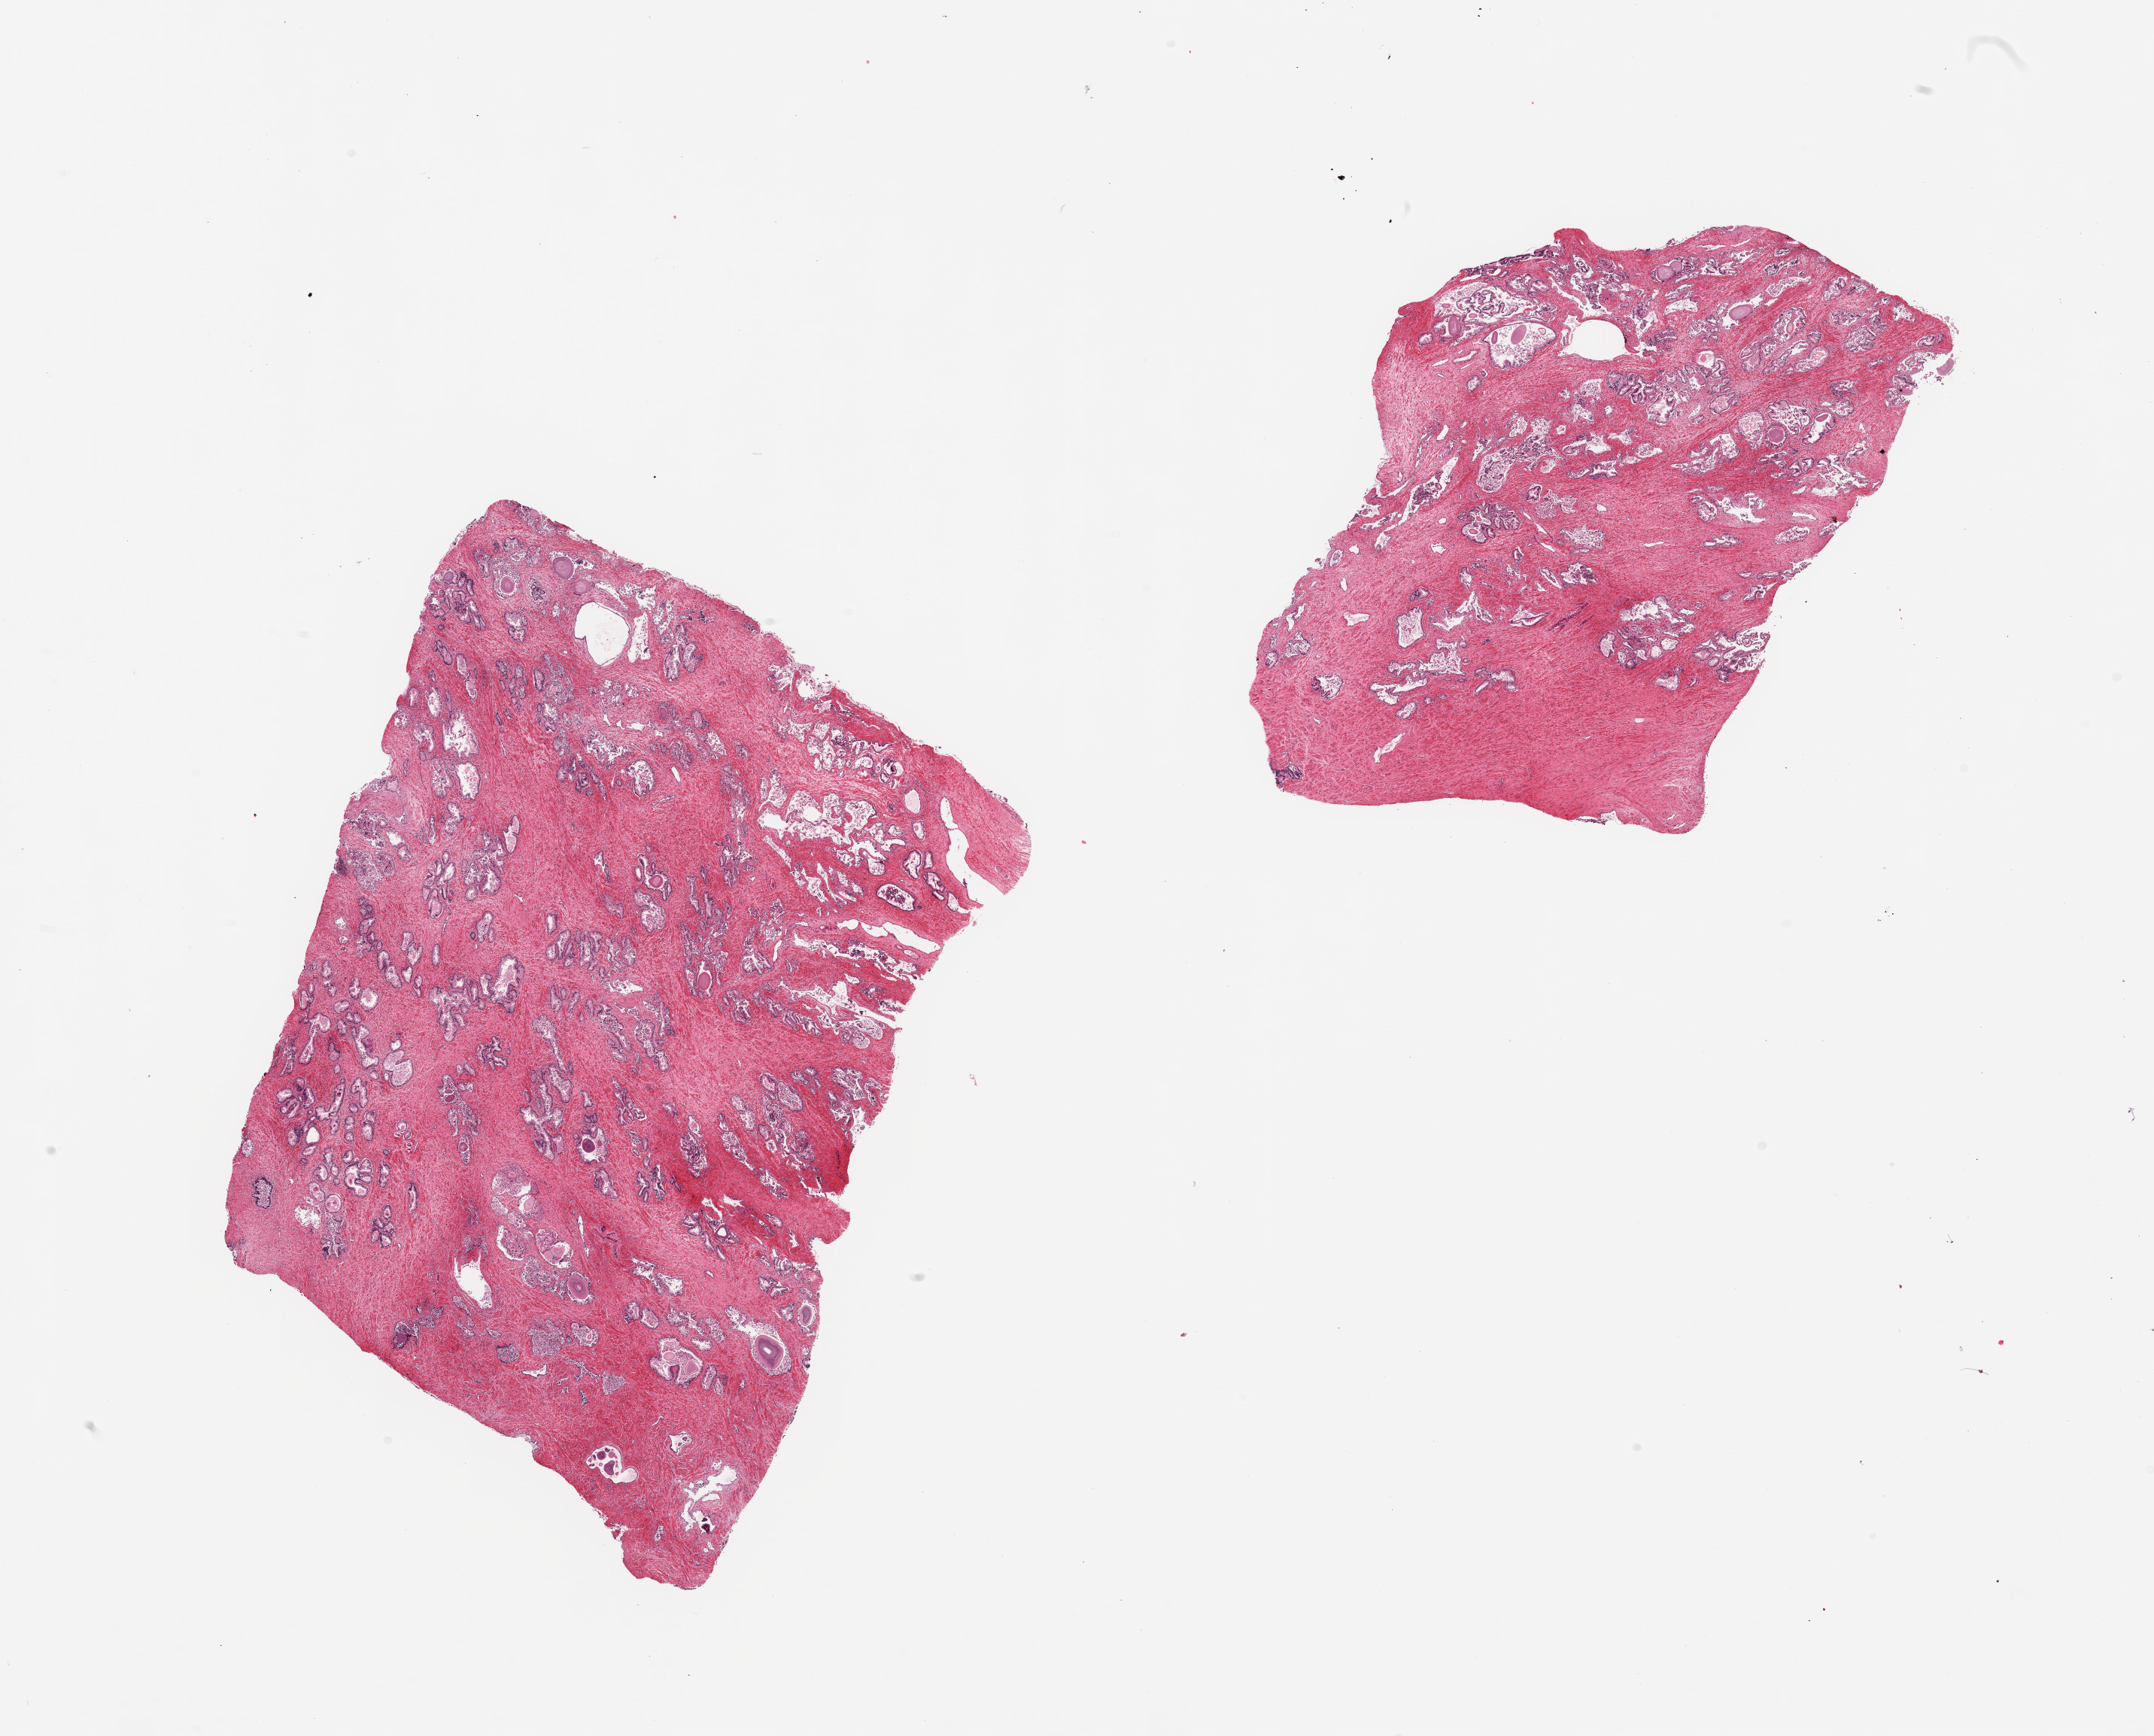
Whole-slide image, haematoxylin and eosin stain — a low-resolution overview of the entire scanned area, about 22.6 x 18.3 mm (acquisition: 20x scan); PAXgene-fixed paraffin-embedded (PFPE) section; sampled site (target tissue): prostate; tissue donor sample. Donor sex: male.
Review note (as recorded): 2 pieces; fibromuscular stroma and glands with partially sloughed epithelium.